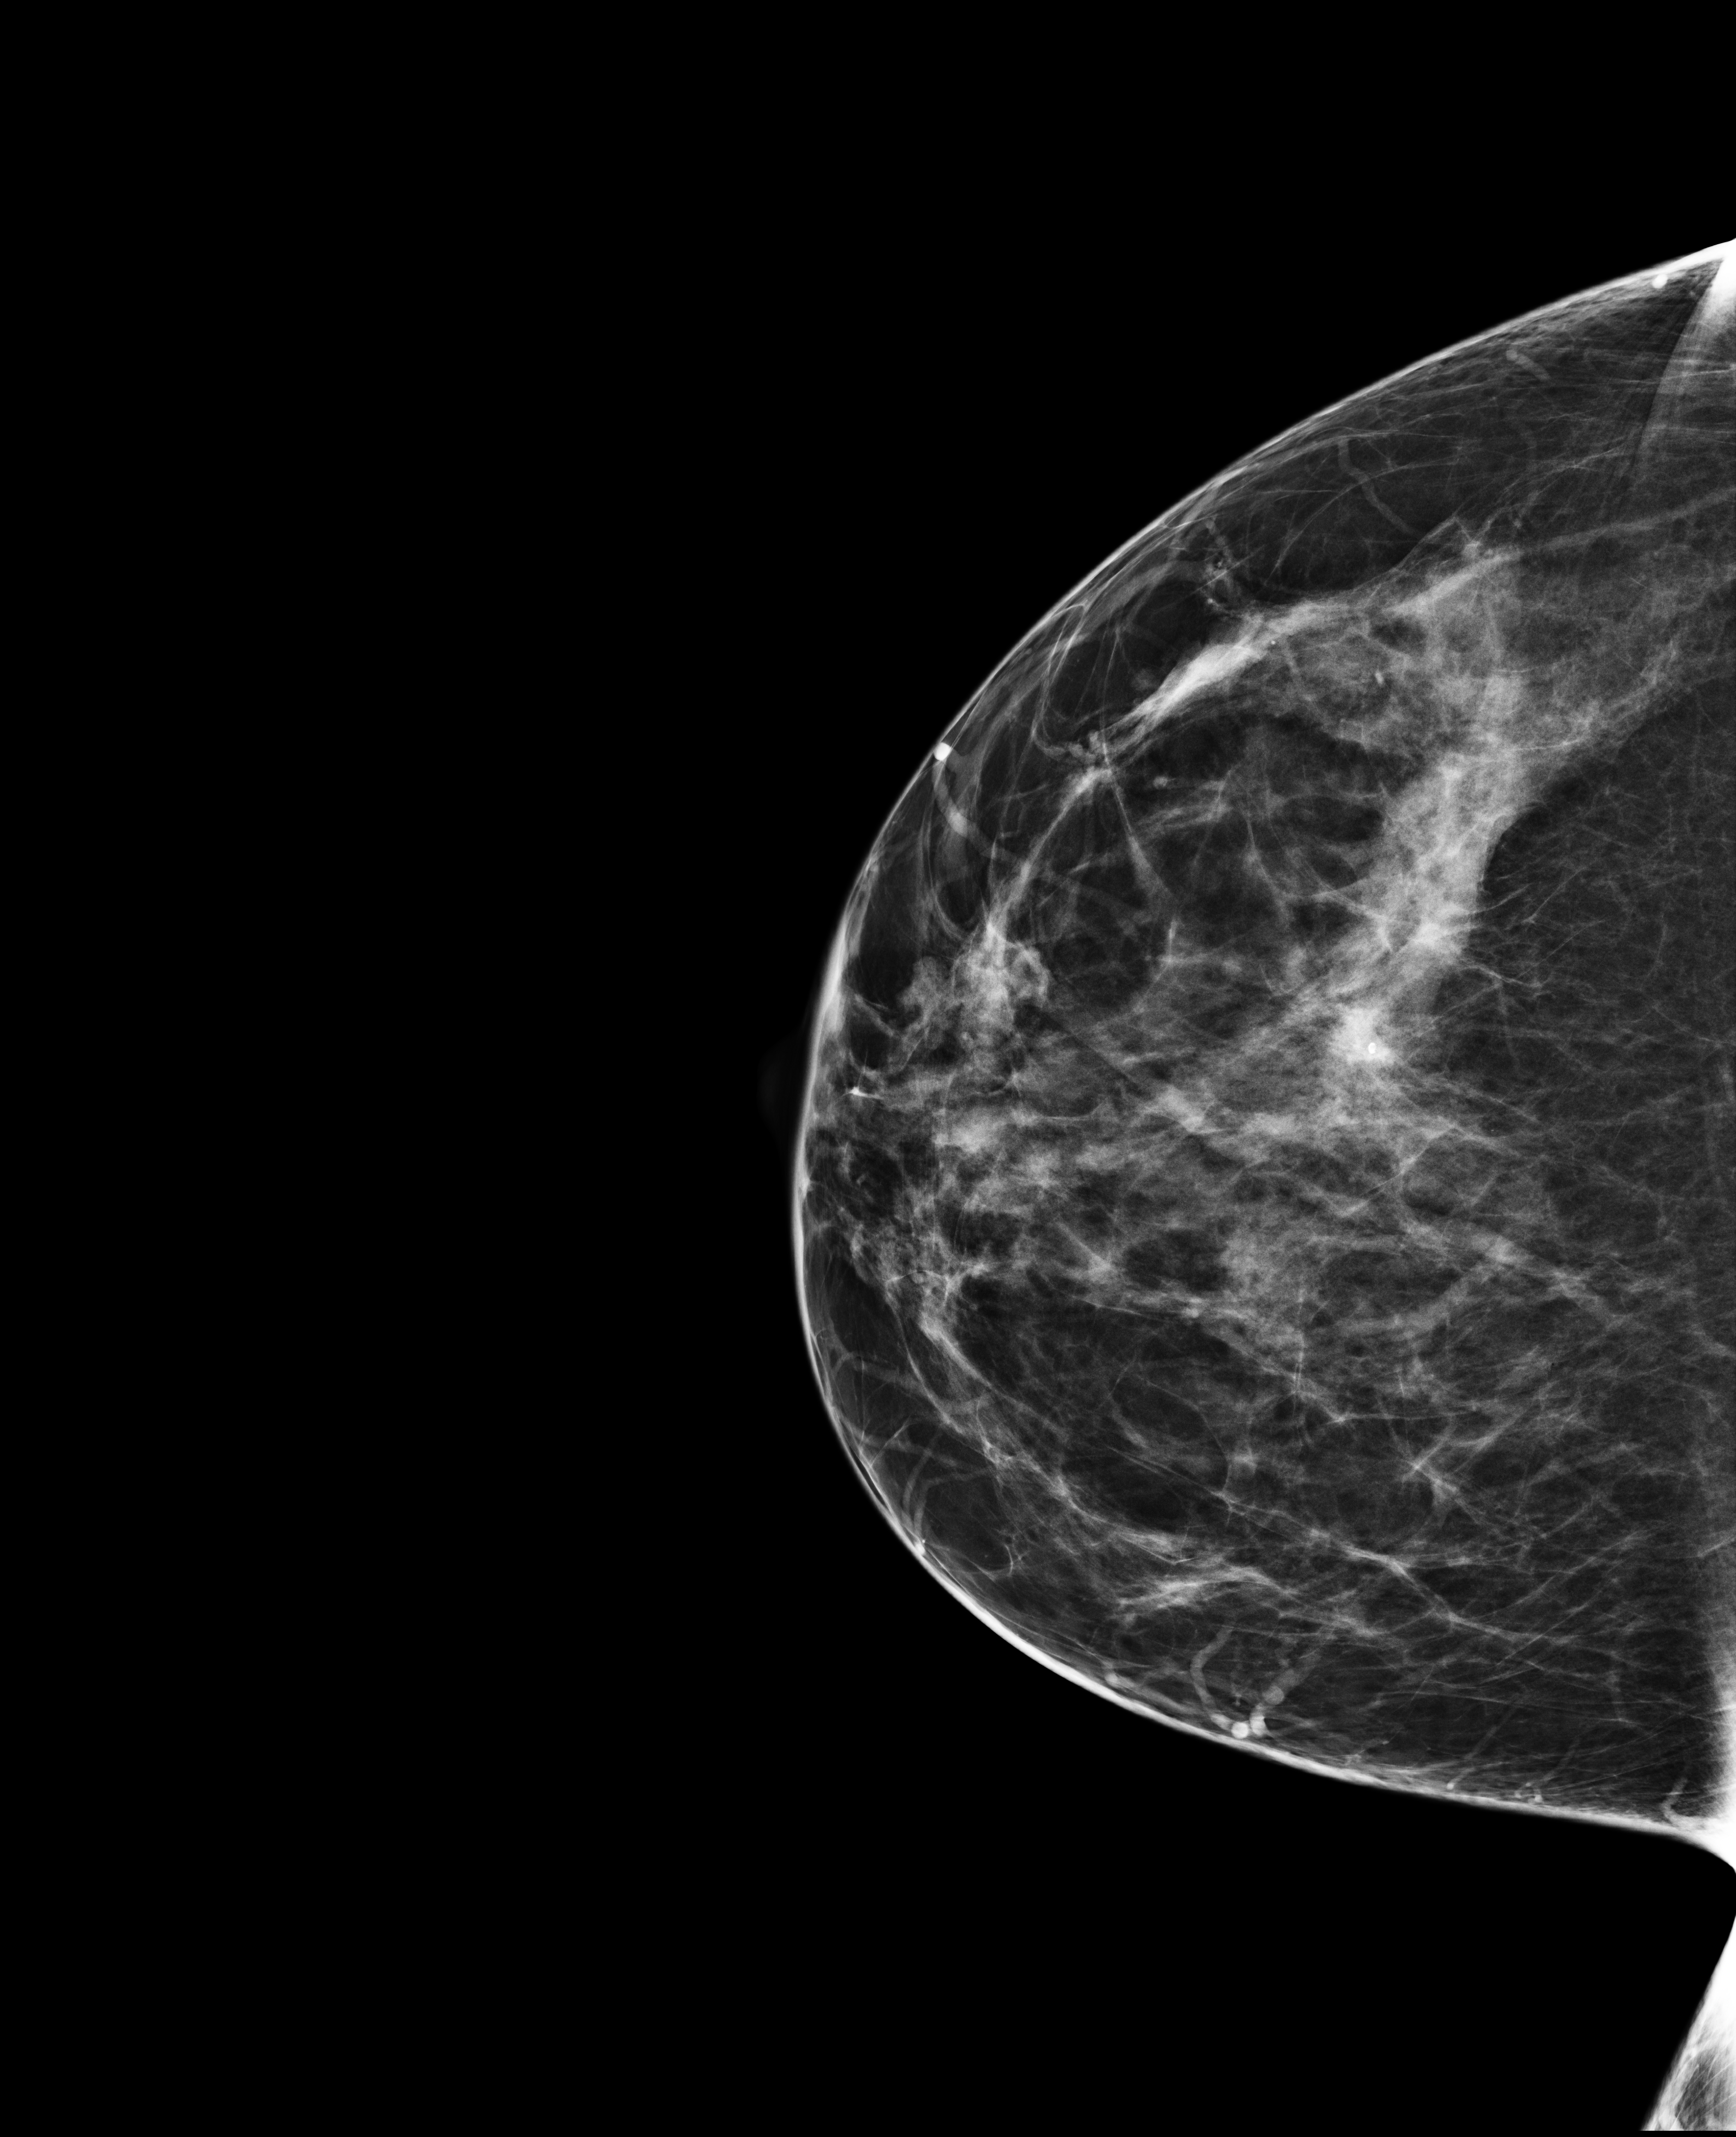
Screening examination, compressed breast thickness 68 mm, system: Selenia Dimensions. Patient aged 48 years (female).
Image type: full-field digital mammogram. Breast: right. Projection: cranio-caudal projection.